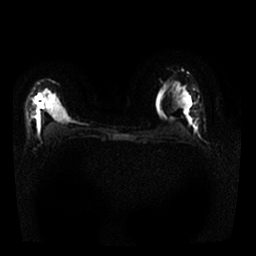
Breast MRI, one axial slice; slice 17 of 25 in the series (ordered by position); diffusion-weighted series; image 2 of 4 stored at this slice position (different b-values; order by instance number); 1.5 T; 256 × 256 image matrix, field of view 320 × 320 mm. Female patient.
Outlined on this slice (manually delineated by an expert):
- tumour on diffusion-weighted imaging: bounding box <36,94,43,107> (left, top, right, bottom; pixels)